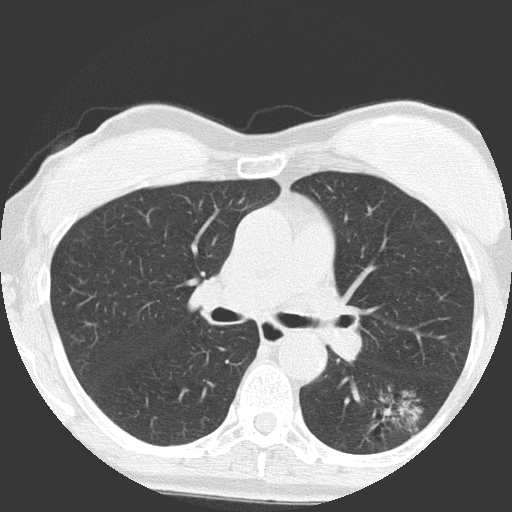
Low-dose screening chest CT, axial slice. First (baseline) screen. Lung window (W 1500 / L -600 HU). Lung (sharp) reconstruction kernel (FC51). Slice 59 of 149 in the series. 512 × 512 image matrix, field of view 300 × 300 mm. Female participant, aged 64 years at enrolment. Former smoker at enrolment.
- Expert reader's lesion annotation, bounding box <346,384,431,457> (left, top, right, bottom; pixels).
- Screening reader's record for this exam (one nodule recorded; not confirmed to be the boxed lesion): non-calcified nodule or mass ≥4 mm, right upper lobe, 4 × 4 mm, poorly defined margins, ground glass attenuation.
- Note: the box lies in the patient's left hemithorax on this image, whereas the reader's record names the right lung; they may be different findings.
- Official screen result: positive, change unspecified: nodule(s) >= 4 mm or enlarging nodule(s), mass(es), or other non-specific abnormalities suspicious for lung cancer.